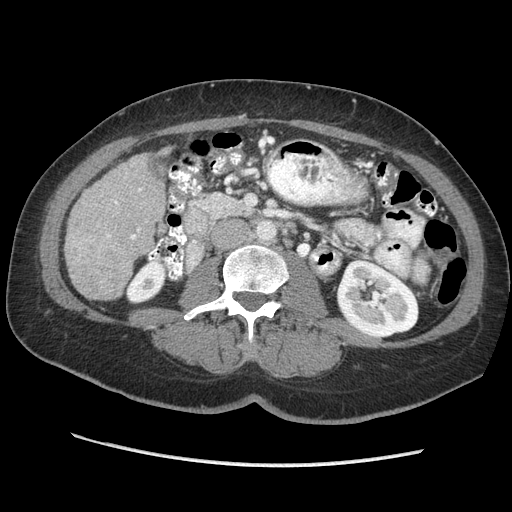
Contrast-enhanced abdominal CT (liver protocol), one axial slice; slice 99 of 170 in the series (ordered by position); reconstruction kernel STANDARD; 140 kVp; soft-tissue window (W 400 / L 40 HU); 2.5 mm slice thickness; 512 × 512 image matrix, field of view 360 × 360 mm. Case-level facts recorded for this patient, not image findings: diagnosis: hepatocellular carcinoma (patient treated with transarterial chemoembolisation; whether this scan precedes or follows treatment is not stated here); TNM stage (as recorded): Stage-II; Child-Pugh class: A.
Structures marked on this image (semi-automatically segmented with operator editing):
- liver parenchyma outside the tumour (the mass and vessels are separate outlines, so this box may not span the whole liver): bounding box (x1, y1, x2, y2) in pixels: (64, 154, 166, 300)
- liver vessels: (107, 188, 142, 239)